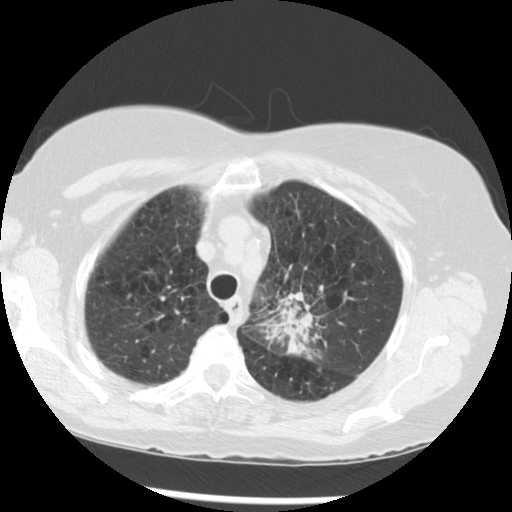
Chest CT (low-dose screening protocol), one axial image, third annual screen, lung window (W 1500 / L -600 HU), 512 × 512 image matrix, field of view 330 × 330 mm. Female participant, aged 70 years at enrolment. Current smoker at enrolment.
• Expert-annotated lung lesion, bounding box [x1, y1, x2, y2] px = [258, 277, 354, 366].
• Reader record for this screening exam (exam-level; its link to the box is not recorded): non-calcified nodule or mass ≥4 mm, left upper lobe, 32 × 26 mm, spiculated (stellate) margins, soft tissue attenuation, pre-existing on the prior screen: yes; interval growth: yes.
• Lung cancer was diagnosed 24 days after this screen: neoplasm, malignant, left upper lobe, stage IIIB (AJCC 6th edition), 40 mm at pathology.